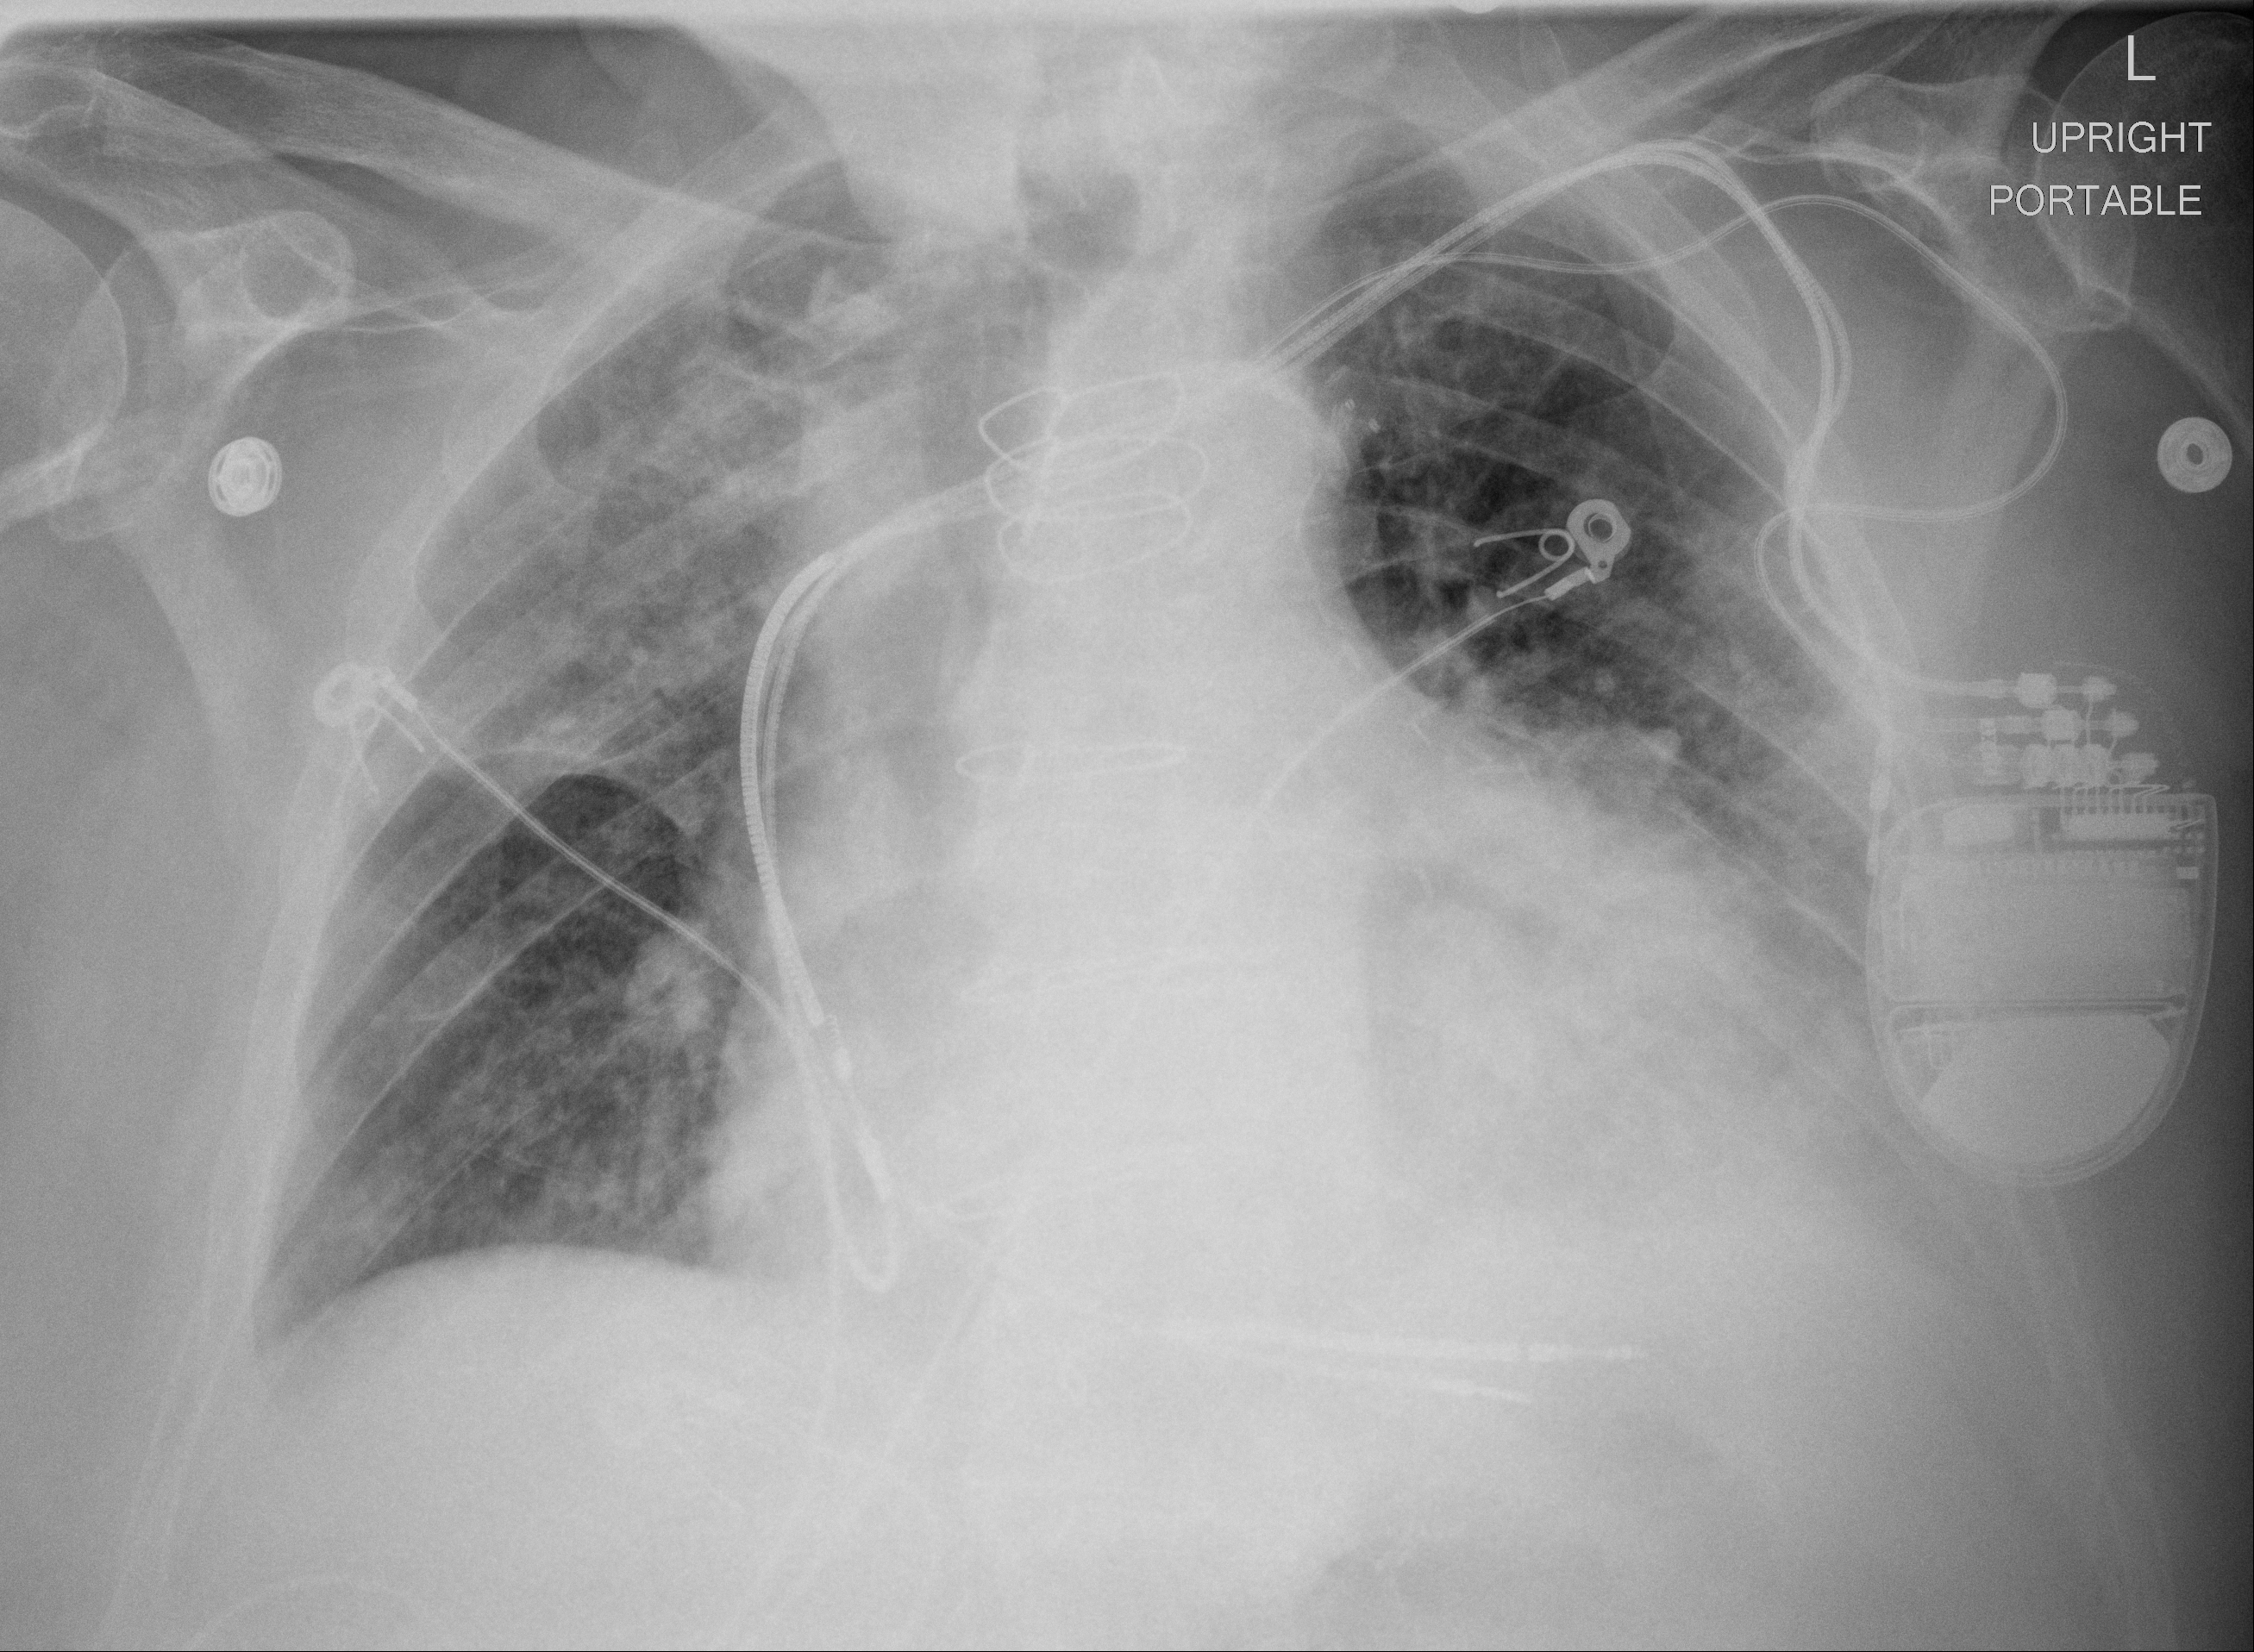
Chest X-ray (portable), AP projection. Male patient, age 87 years; imaged 5 days after the COVID-19 diagnosis.
Key findings recorded by the radiologist: Increased left pleural effusion with consolidation and/or atelectasis in the left lower lobe.